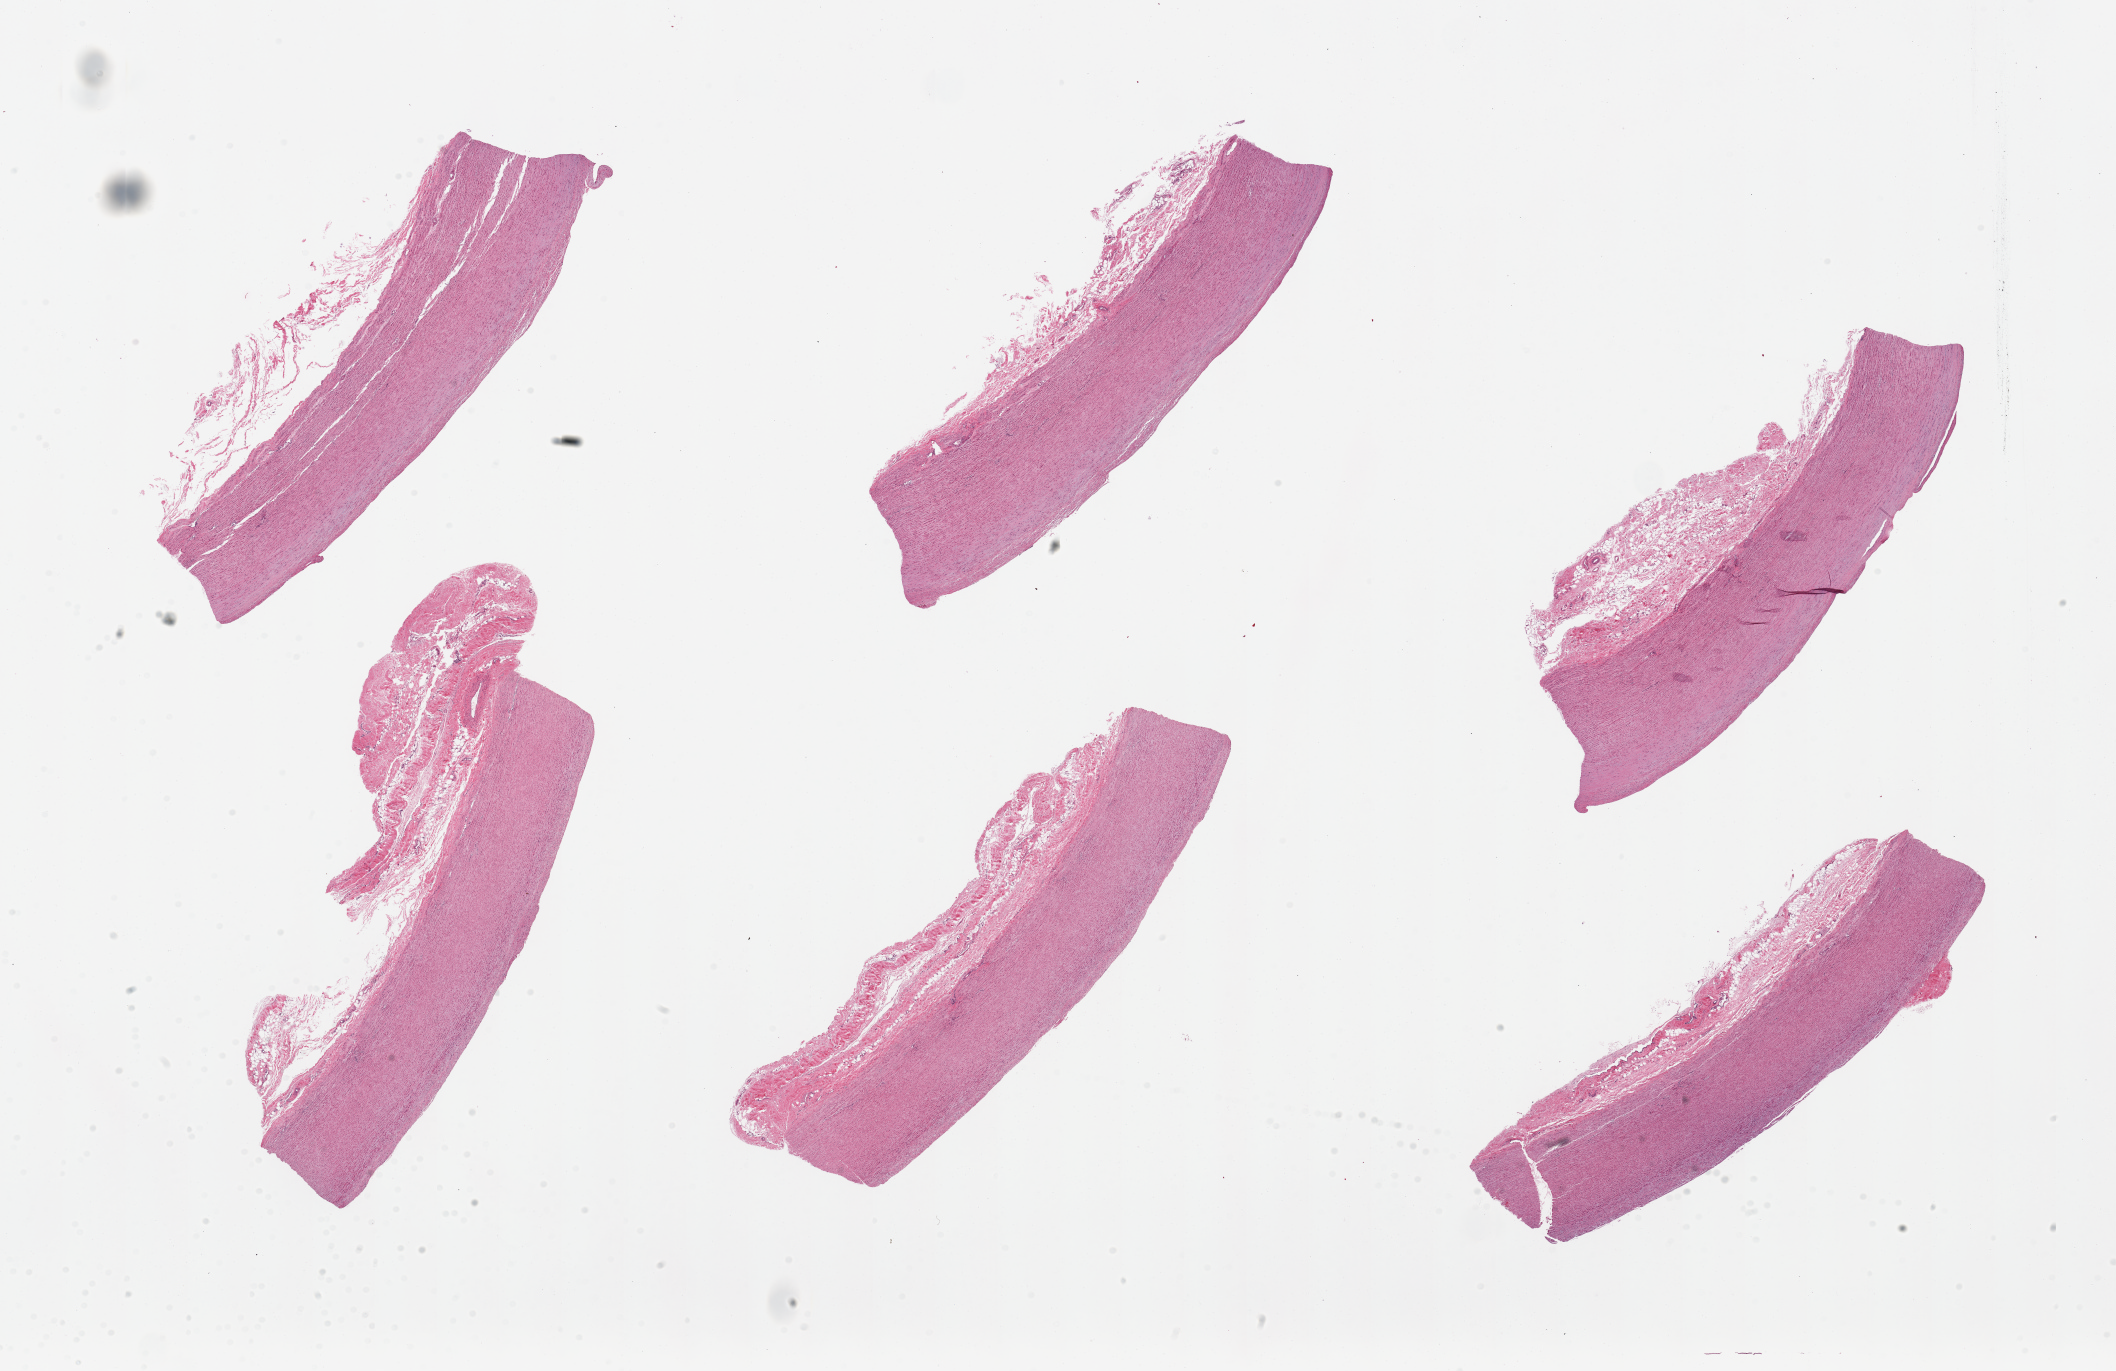
Whole-slide image, H&E stain, low-resolution overview of the scanned area, about 33.5 x 21.7 mm (acquisition: 20x scan), PAXgene-fixed, paraffin-embedded tissue, target tissue: aorta, donor tissue sample. Donor: male.
- reviewer comment on this tissue sample: 6 pieces, up to 11x4mm